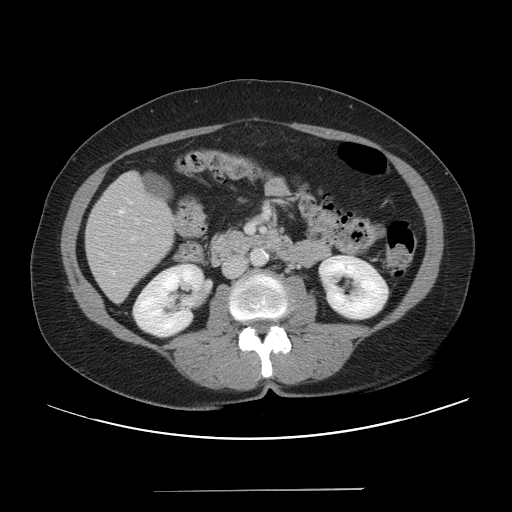
Contrast-enhanced abdominal CT, one axial slice; 120 kVp; intravenous contrast given; soft-tissue window (W 400 / L 40 HU); 5 mm slice thickness; 512 × 512 image matrix, field of view 419 × 419 mm. Female patient, age 54 years. Case-level facts recorded for this patient, not image findings: diagnosis: colorectal cancer liver metastases, imaged before liver resection; multiple liver metastases: yes; largest metastasis: 3.2 cm; disease in both lobes: yes.
Annotated regions visible in this slice (outlined manually by an expert reader):
- liver: bounding box [x1, y1, x2, y2] px = [87, 173, 174, 301]
- portal vein (with intrahepatic branches): [247, 225, 254, 232]